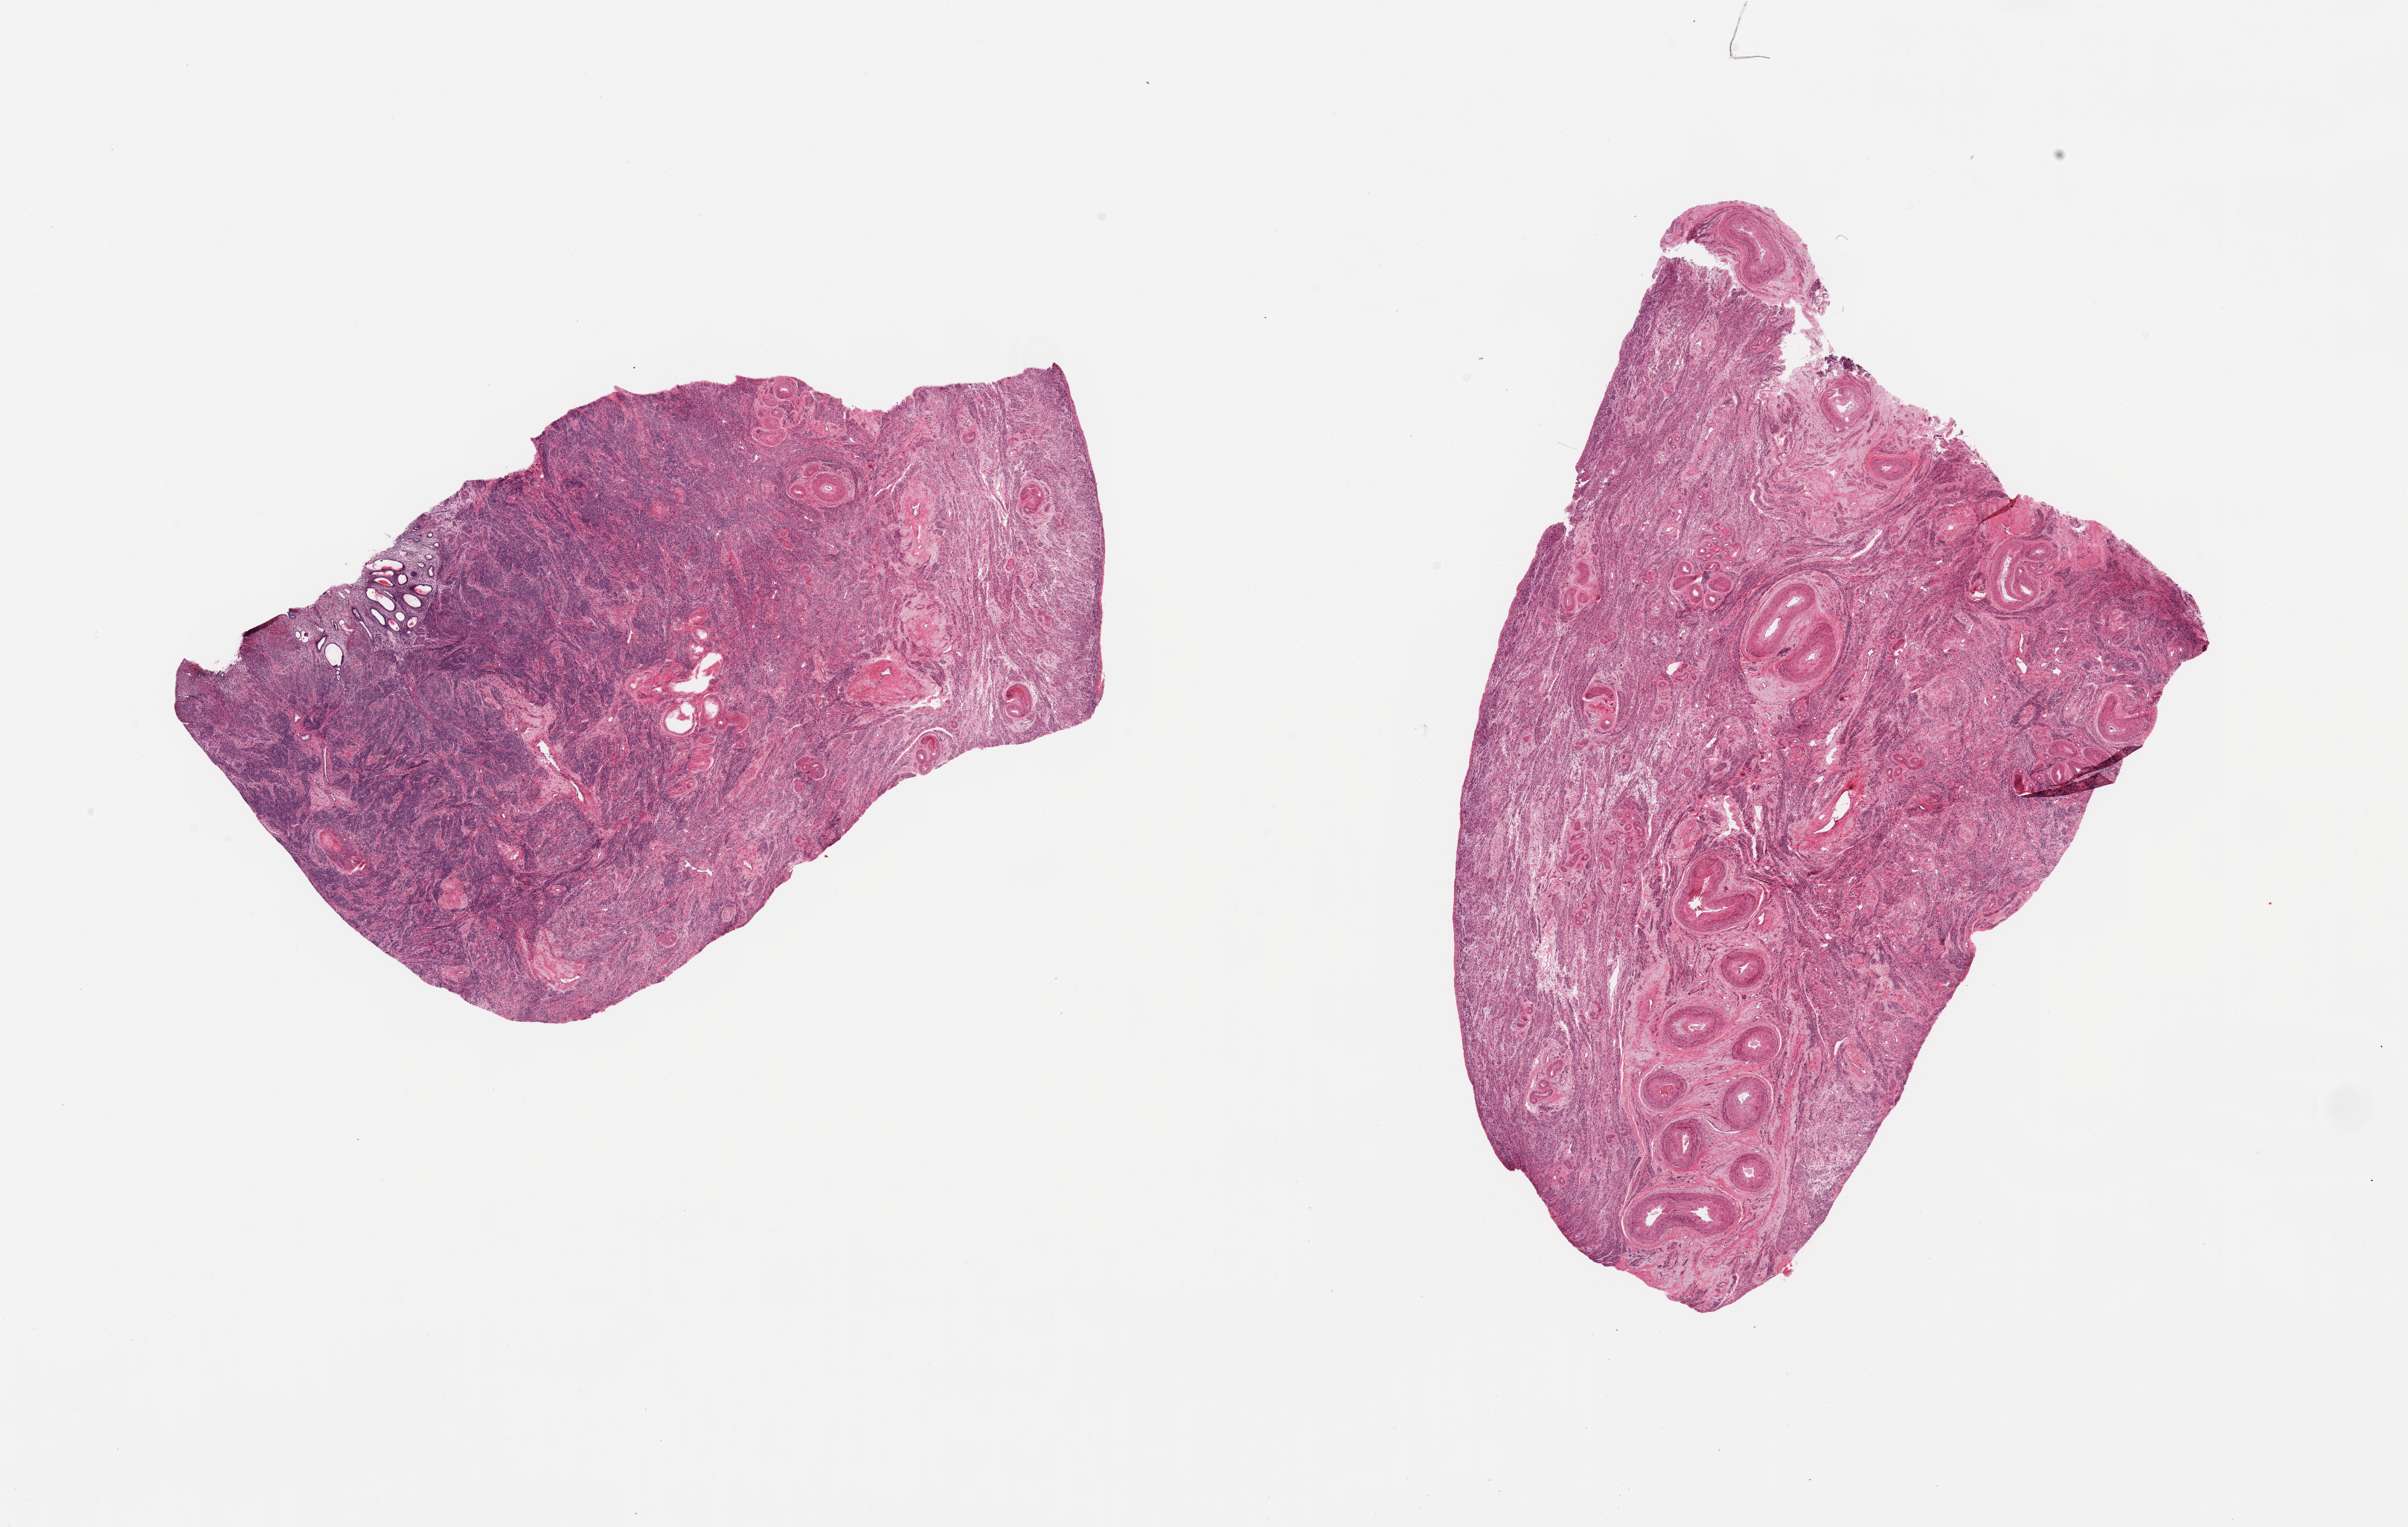
Whole-slide image, hematoxylin and eosin (H&E) stain, whole scanned area (about 25.6 x 16.2 mm, acquisition: 20x scan) shown as a low-resolution overview. PAXgene-fixed paraffin-embedded (PFPE) section. Sampled site (target tissue): uterus. Tissue donor sample. Donor: female.
Reviewer comment on this tissue sample: 2 pieces; small focus of atrophic endometrium in 1 piece; mostly myometrium with high vascular content in 1 piece.